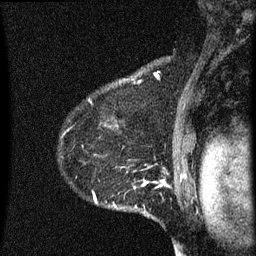
Breast MRI (dynamic contrast-enhanced), one sagittal slice. Slice 49 of 60 in the series (ordered by position). Dynamic contrast-enhanced series, image 2 of 3 at this slice position (ordered by acquisition). 1.5 T. TE 4.2 ms, TR 8 ms. 256 × 256 image matrix, field of view 180 × 180 mm. Patient: female, 55 years.
Annotated regions visible in this slice (semi-automatic segmentation, software-assisted and operator-edited):
- analysis volume of interest (the breast-tissue region the enhancement analysis was run in; not a lesion): bounding box <59,156,145,215> (left, top, right, bottom; pixels)
- tumour enhancement mask (voxels above the 70 % enhancement threshold inside the analysis volume of interest): <94,184,145,213>